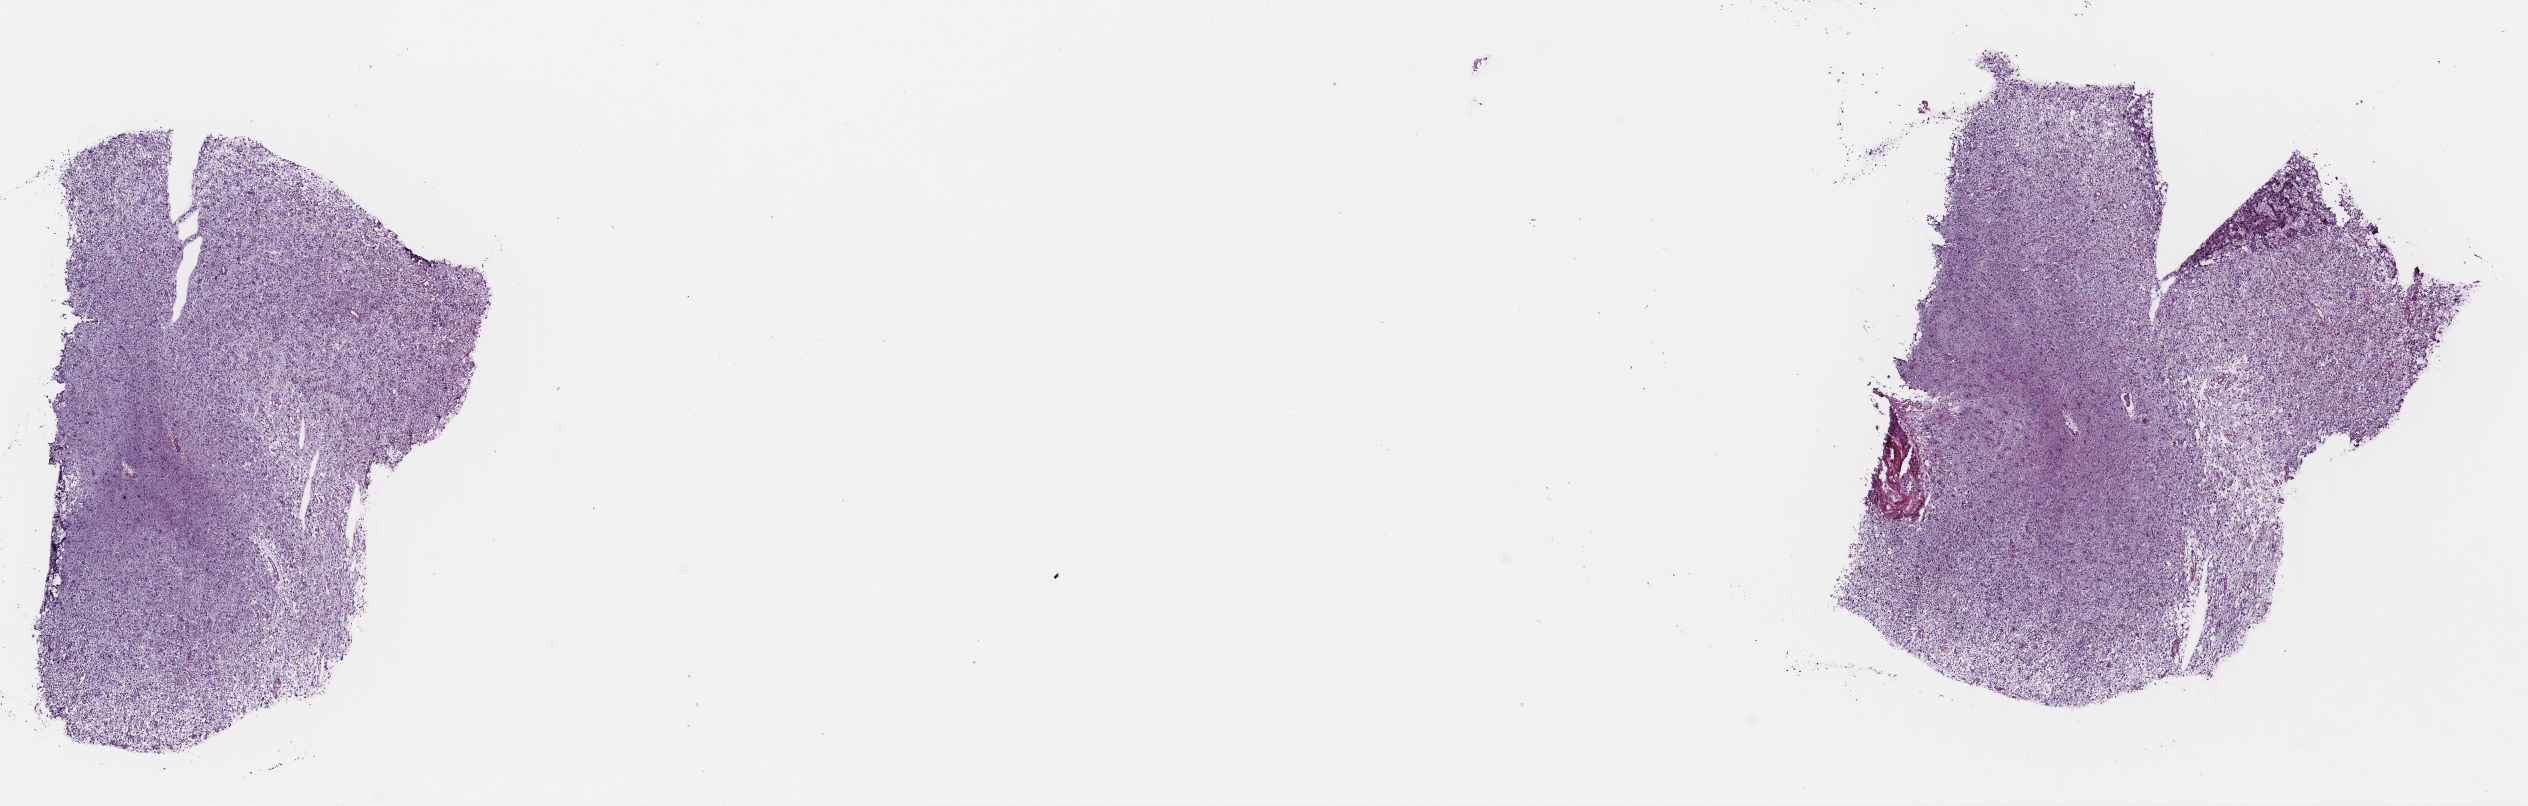
Digitized H&E tissue section (whole slide), whole scanned area (about 19.9 x 6.3 mm, slide scanned at 40x) shown as a low-resolution overview. Frozen section. Primary tumour sample from the brain. Patient: male, age at initial diagnosis 52 years. Histologic grade: G3 (poorly differentiated). Slide review estimates, as recorded: tumour cells 50%, tumour nuclei 80%, normal cells 10%, stromal cells 40%, necrosis 0%. Inflammatory infiltration, as recorded: lymphocyte infiltration 0%, monocyte infiltration 0%, neutrophil infiltration 0%.
Pathologic diagnosis: Astrocytoma, anaplastic (cerebrum).